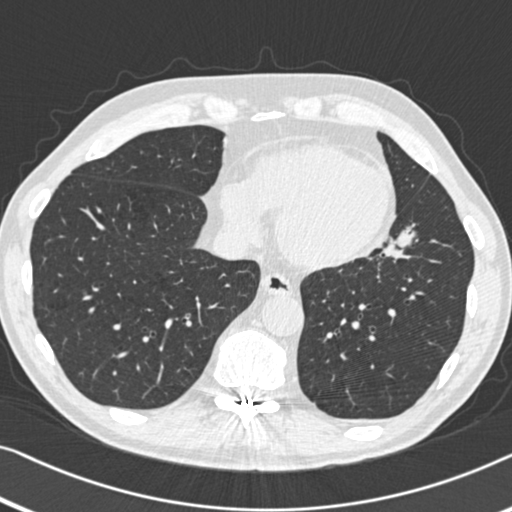
Low-dose screening chest CT, one axial slice; slice 140 of 383 in the series (ordered by position); 120 kVp; lung window (W 1500 / L -600 HU); 512 × 512 image matrix, field of view 332 × 332 mm.
Annotated regions visible in this slice (expert manual segmentation):
- lesion 1 (tumor, upper lobe of left lung): bounding box (x1, y1, x2, y2) in pixels: (382, 226, 416, 259)